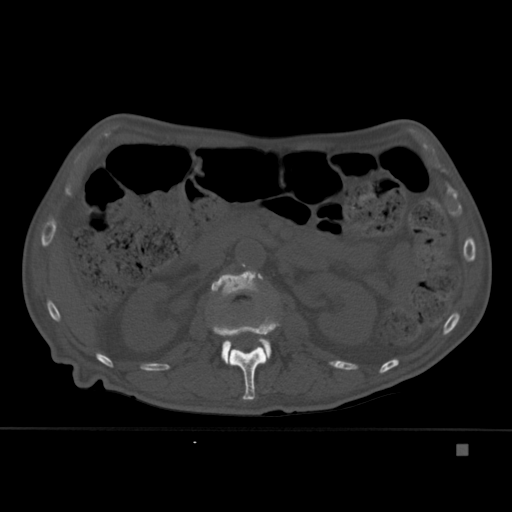
CT including the spine, one axial slice; slice 175 of 451 in the series (ordered by position); bone window (W 1800 / L 400 HU); 1.5 mm slice thickness; 512 × 512 image matrix, field of view 378 × 378 mm. Patient: male, 75 years. From the clinical record (not read from this slice): primary cancer: prostate.
Annotated regions visible in this slice (semi-automatic segmentation, software-assisted and operator-edited):
- L1 vertebra: bounding box [x1, y1, x2, y2] px = [213, 317, 279, 400]
- L2 vertebra: [211, 270, 272, 364]